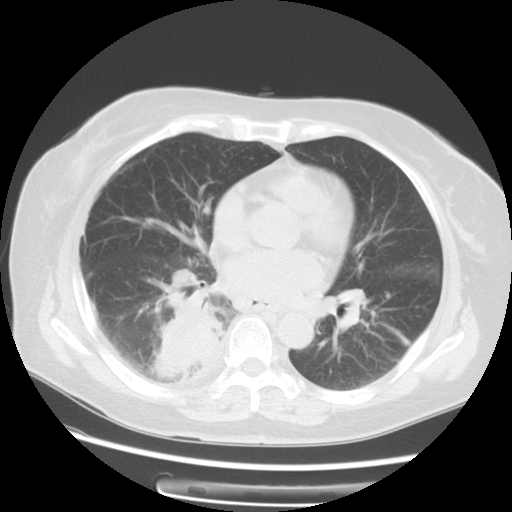
Chest CT, one axial slice. Position 29 of 57 along the scan axis. Reconstruction kernel STANDARD. 120 kVp. Lung window (W 1500 / L -600 HU). 5 mm slice thickness. 512 × 512 image matrix, field of view 350 × 350 mm. Patient: female, 69 years. From the clinical record (not read from this slice): clinical TNM (as recorded): T2 N1 M1a.
Outlined on this slice (bounding box drawn by a radiologist):
- lung tumour (recorded histology: adenocarcinoma): bounding box [x1, y1, x2, y2] px = [154, 298, 225, 391]